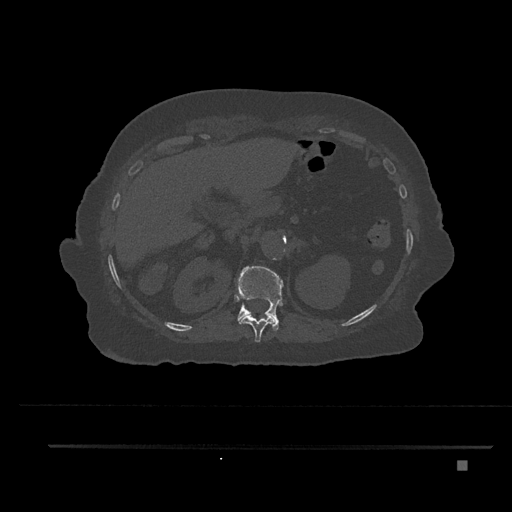
CT including the spine, one axial slice; slice 286 of 797 in the series (ordered by position); bone window (W 1800 / L 400 HU); 0.5 mm slice thickness; 512 × 512 image matrix, field of view 437 × 437 mm. Patient: female, 76 years. From the clinical record (not read from this slice): primary cancer: lung.
Structures marked on this image (semi-automatically segmented with operator editing):
- T11 vertebra: box from (x=237, y=273) to (x=275, y=342) px
- T12 vertebra: (x=236, y=265)–(x=283, y=331)